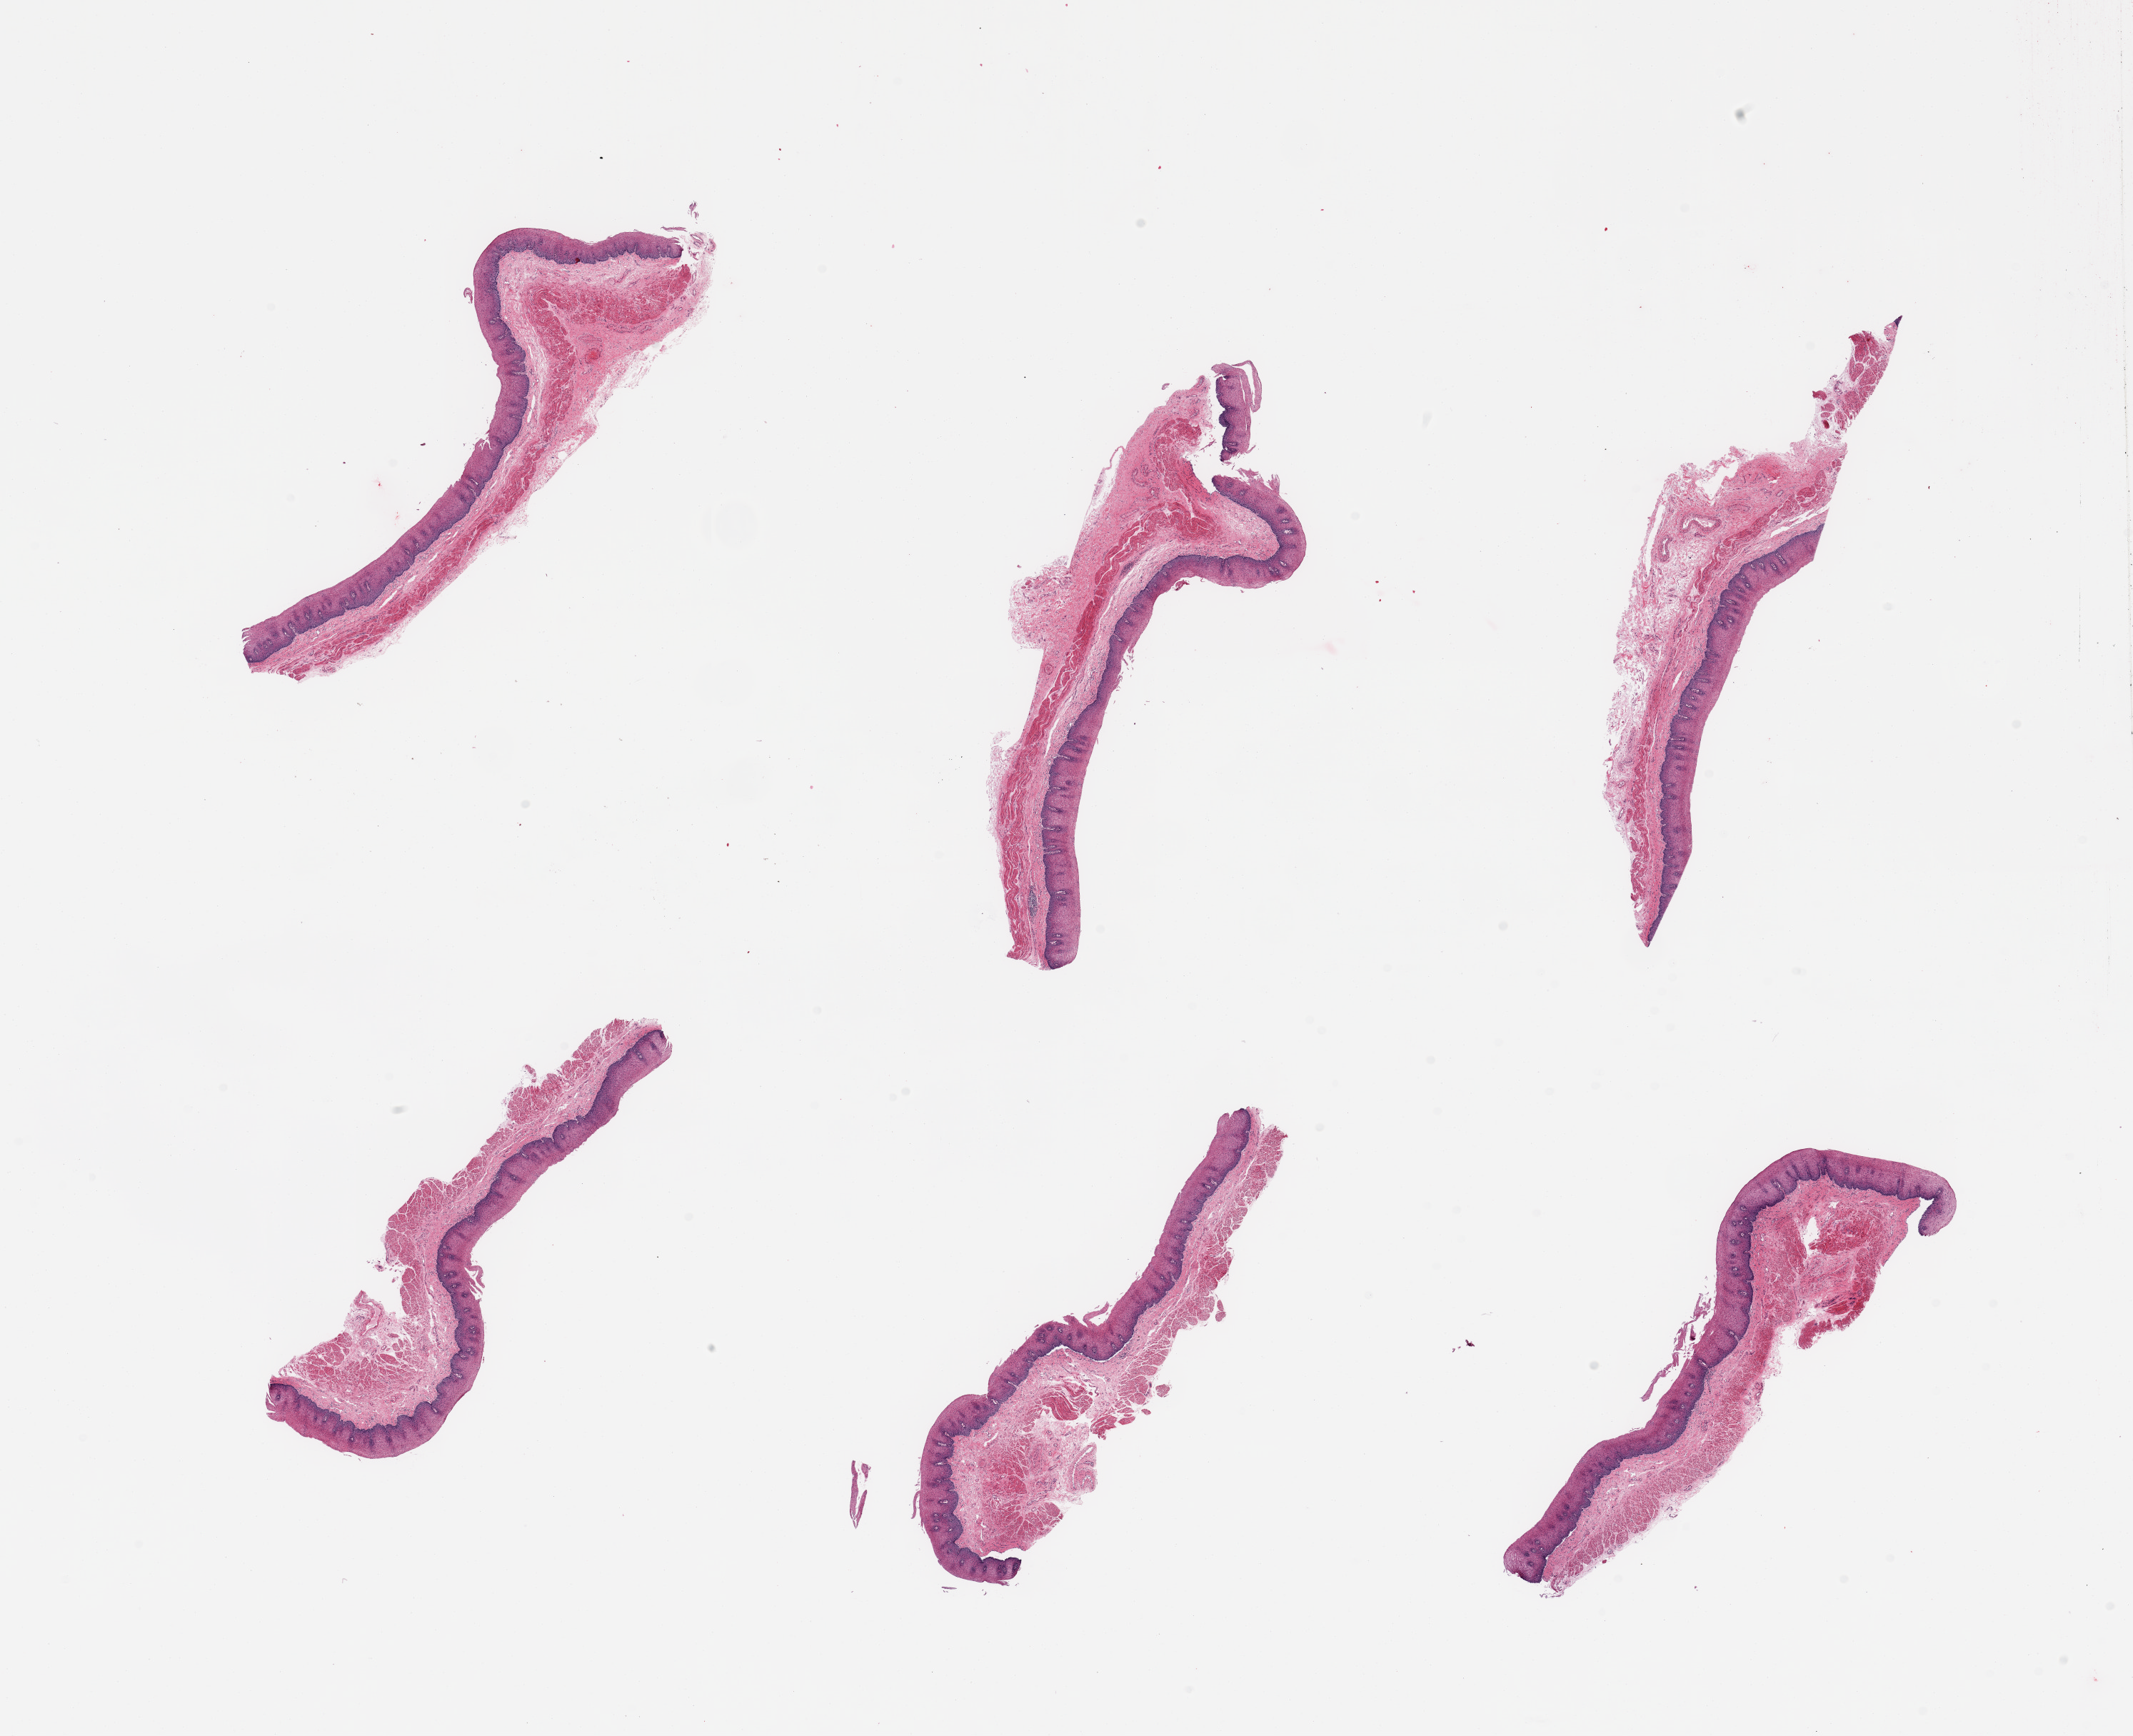
Whole-slide image, H&E stain, brightfield, low-resolution overview of the scanned area, about 23.6 x 19.2 mm. PAXgene-fixed paraffin-embedded (PFPE) section. Sampled site (target tissue): esophageal mucous membrane. Tissue donor sample. Donor sex: male.
Review note (as recorded): 6 pieces, squamous mucosa up to ~0.35mm, ~40-50% thickness.